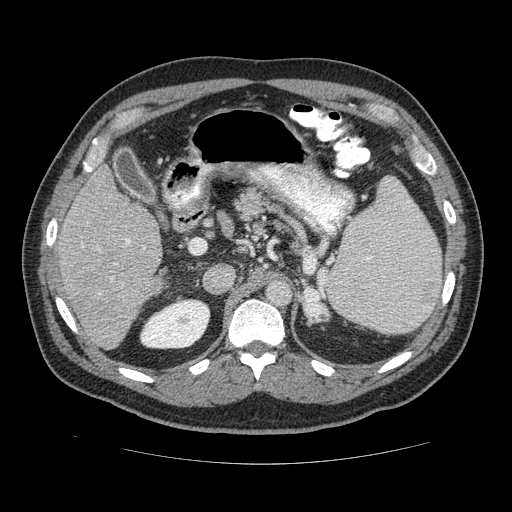
Contrast-enhanced abdominal CT (liver protocol), one axial slice. Position 75 of 113 along the scan axis. 120 kVp. Soft-tissue window (W 400 / L 40 HU). 2.5 mm slice thickness. 512 × 512 image matrix. Case-level facts recorded for this patient, not image findings: diagnosis: hepatocellular carcinoma (patient treated with transarterial chemoembolisation; whether this scan precedes or follows treatment is not stated here); TNM stage (as recorded): Stage-II; Child-Pugh class: B; tumour differentiation: moderately differentiated; tumour nodularity: multinodular.
Annotated regions visible in this slice (semi-automatically segmented with operator editing):
- liver parenchyma outside the tumour (the mass and vessels are separate outlines, so this box may not span the whole liver): bounding box [x1, y1, x2, y2] px = [52, 164, 171, 350]
- liver vessels: [82, 239, 144, 298]